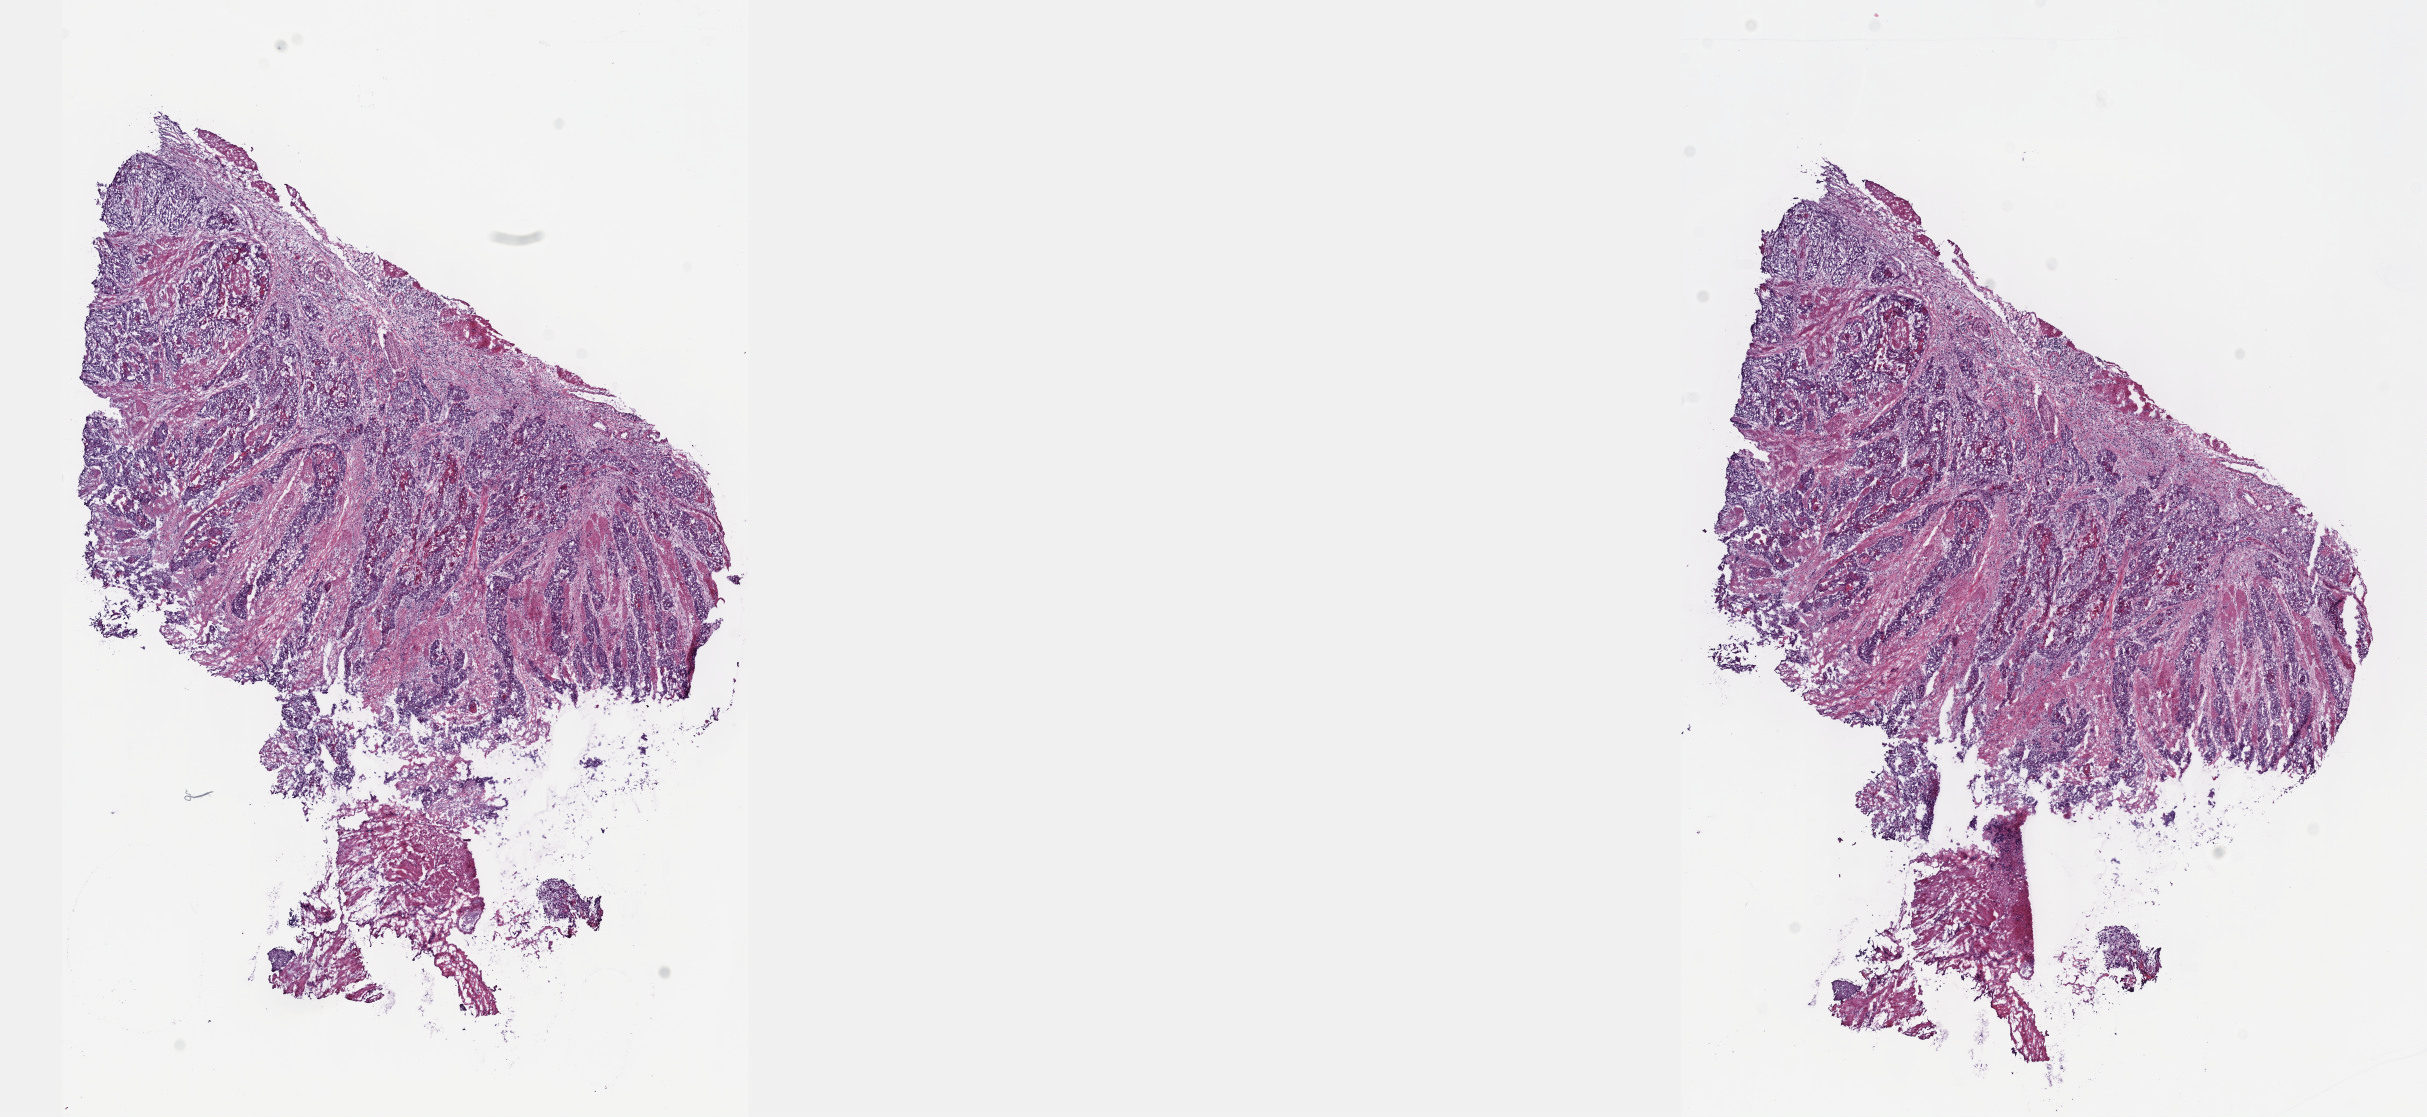
H&E whole-slide image, shown as a low-resolution overview of the whole scanned area (about 19.6 x 9.0 mm); frozen section from the top of the tissue portion; primary tumour sample from the esophagus. Female, age 84 years at initial diagnosis. Histologic grade: G1 (well differentiated). Slide review estimates, as recorded: tumour cells 90%, tumour nuclei 60%, normal cells 5%, stromal cells 0%, necrosis 5%. Infiltration values recorded for this section: lymphocyte infiltration 0%, monocyte infiltration 0%, neutrophil infiltration 0%.
* AJCC pathologic stage: IIA (6th edition)
* lymph nodes positive (case pathology): 0 of 14 examined
* pathologic diagnosis: Squamous cell carcinoma, NOS (middle third of esophagus)